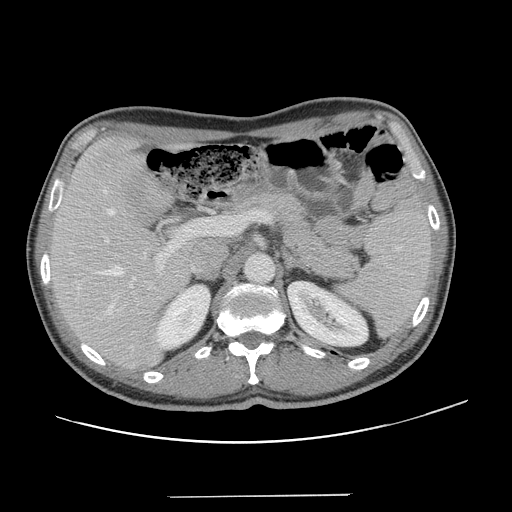
Contrast-enhanced abdominal CT, one axial slice. Position 83 of 131 along the scan axis. 120 kVp. Intravenous contrast given. Soft-tissue window (W 400 / L 40 HU). 512 × 512 image matrix. Male patient, age 60 years. From the clinical record (not read from this slice): diagnosis: colorectal cancer liver metastases, imaged before liver resection; multiple liver metastases: no; largest metastasis: 2.5 cm; disease in both lobes: no.
Outlined on this slice (manually delineated by an expert):
- hepatic veins: bounding box (x1, y1, x2, y2) in pixels: (96, 190, 146, 315)
- liver: (51, 138, 190, 366)
- planned liver remnant (the part of the liver to remain after resection): (51, 138, 190, 356)
- portal vein (with intrahepatic branches): (105, 219, 214, 288)